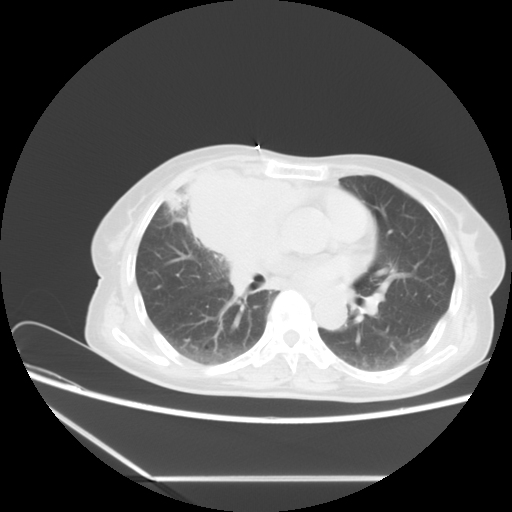
Chest CT, one axial slice. Slice 6 of 16 in the series (ordered by position). Reconstruction kernel STANDARD. Lung window (W 1500 / L -600 HU). 5 mm slice thickness. 512 × 512 image matrix. Female patient, age 63 years. Case-level facts recorded for this patient, not image findings: clinical TNM (as recorded): T2b N1 M0.
Annotated regions visible in this slice (rectangle marked by the reading radiologist):
- lung tumour (recorded histology: adenocarcinoma): bounding box [x1, y1, x2, y2] px = [181, 146, 313, 260]